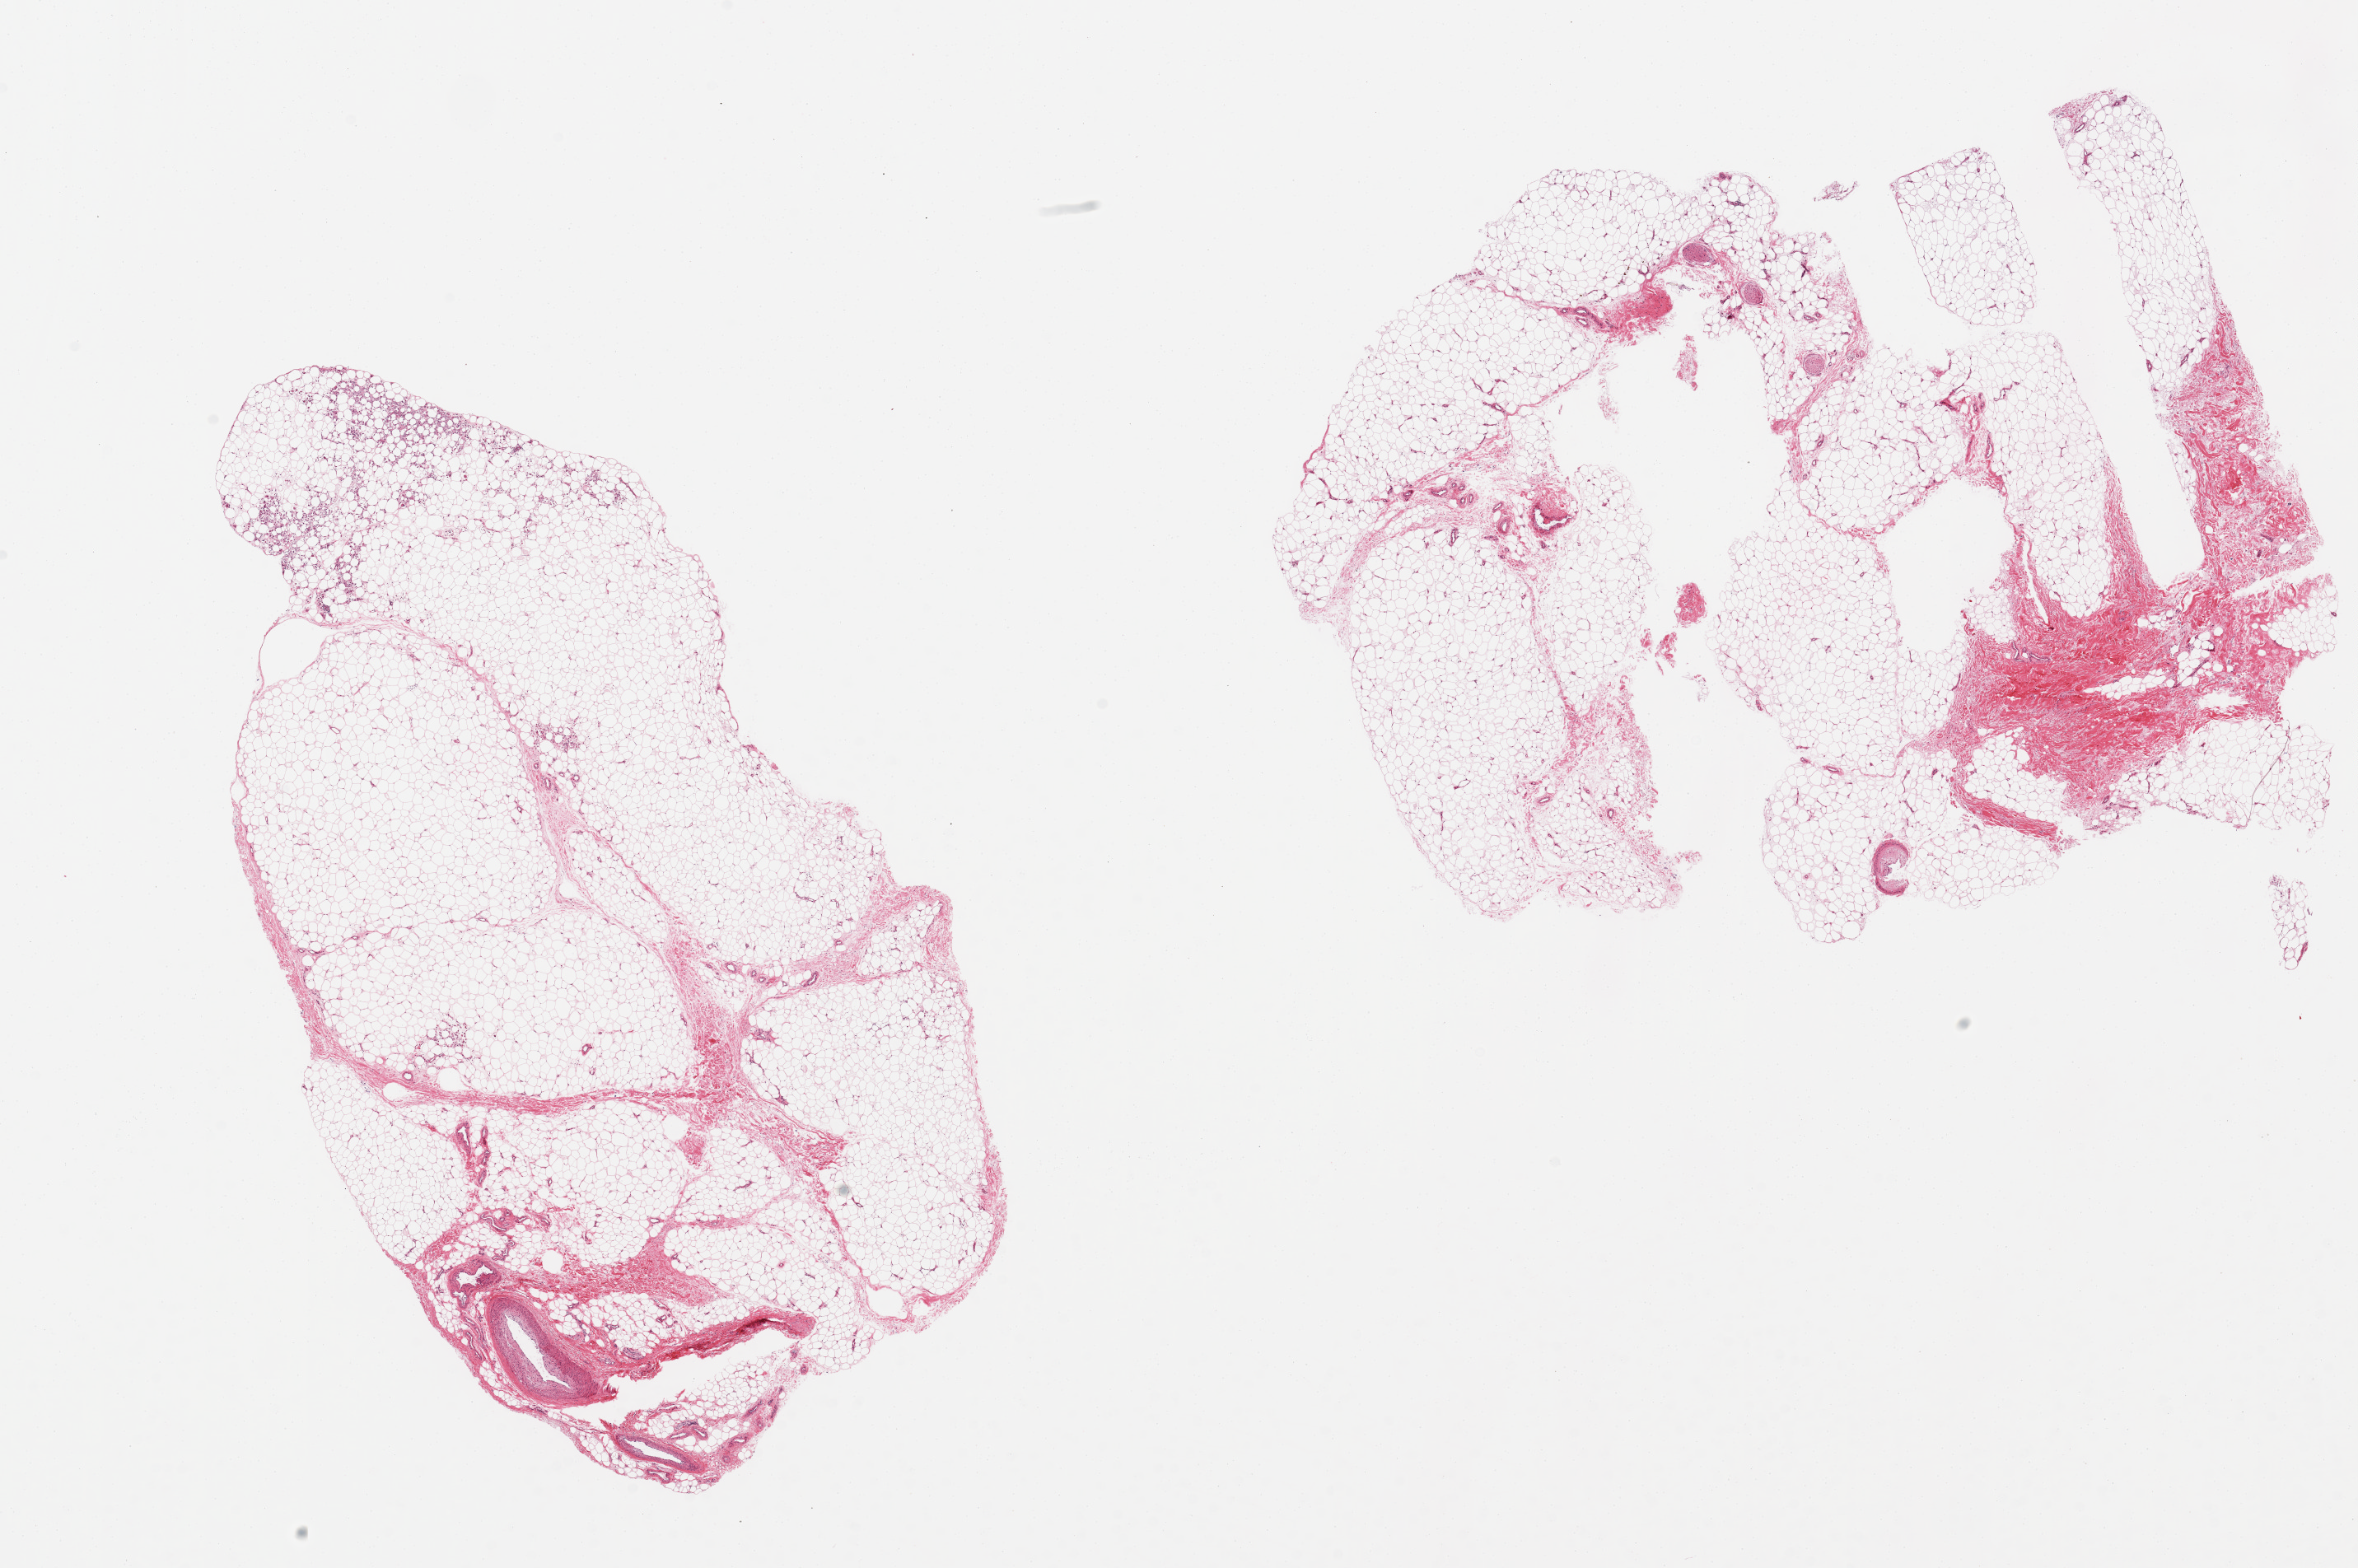
Digitized H&E-stained section, whole scanned area (about 22.6 x 15.1 mm) shown as a low-resolution overview; PAXgene-fixed, paraffin-embedded tissue; section of adipose tissue (target tissue); donor tissue sample.
Reviewer comment on this tissue sample: 2 pieces.